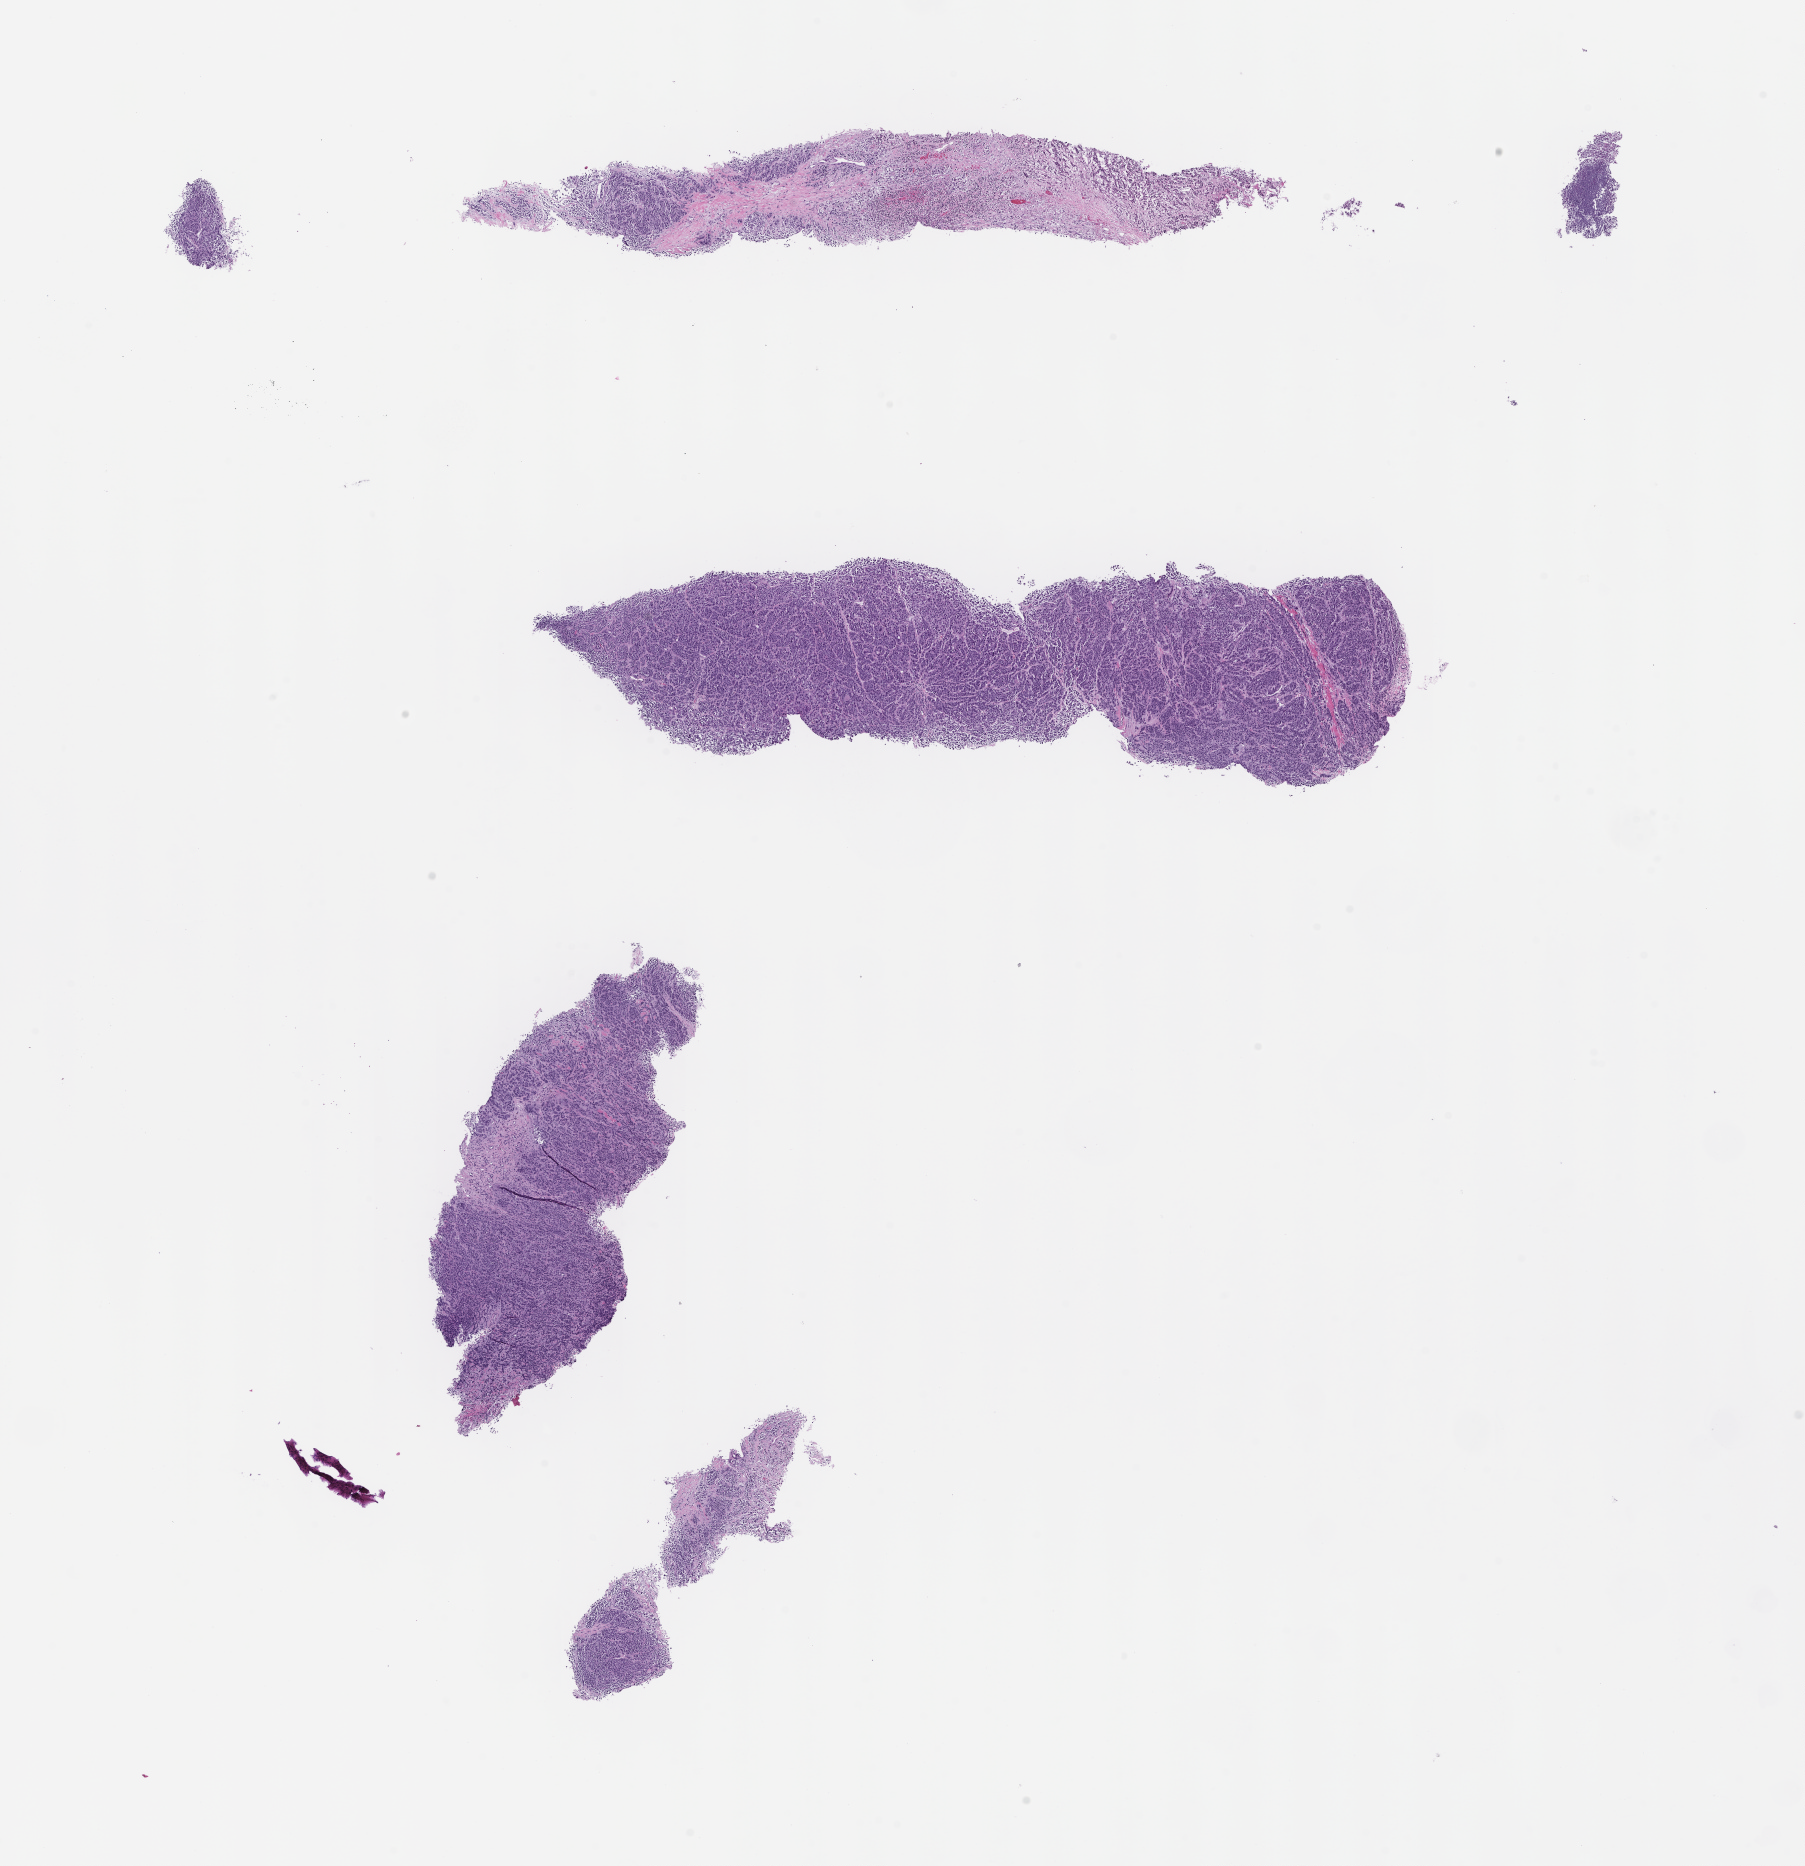
Whole-slide image, hematoxylin and eosin (H&E) stain, low-resolution overview of the scanned area, about 14.6 x 15.1 mm. FFPE section. Patient sex: female.
* this section: metastatic tumor tissue
* primary diagnosis of the patient: Melanoma